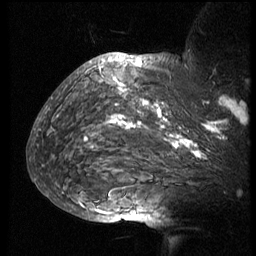
Breast MRI (dynamic contrast-enhanced), one sagittal slice; position 53 of 74 along the scan axis; 3 images stored at this slice position (order not interpretable as contrast timing); 1.5 T; TE 4.2 ms, TR 8.9 ms; 2.5 mm slice thickness; 256 × 256 image matrix, field of view 200 × 200 mm. Female patient, age 57 years. Case-level facts recorded for this patient, not image findings: setting: breast cancer imaged before/during neoadjuvant chemotherapy; receptor status: HER2-positive.
Outlined on this slice (semi-automatically segmented with operator editing):
- analysis volume of interest (the breast-tissue region the enhancement analysis was run in; not a lesion): bounding box [x1, y1, x2, y2] px = [51, 67, 249, 173]
- tumour enhancement mask (voxels above the 140 % enhancement threshold inside the analysis volume of interest): [86, 79, 247, 159]